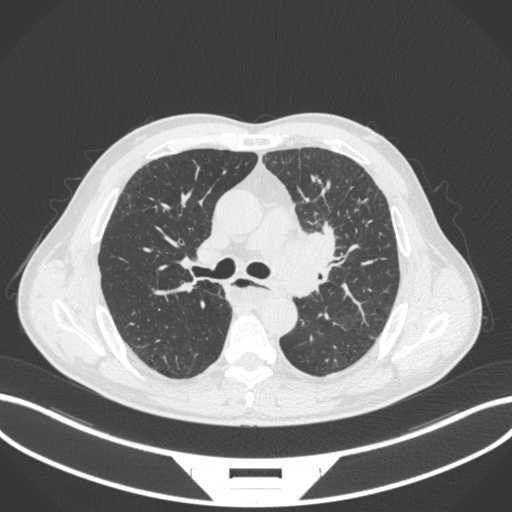
Chest CT, one axial slice; slice 239 of 411 in the series (ordered by position); 120 kVp; lung window (W 1500 / L -600 HU); 512 × 512 image matrix, field of view 400 × 400 mm. Male patient, age 57 years. Case-level facts recorded for this patient, not image findings: clinical TNM (as recorded): T2a N1 M0.
Annotated regions visible in this slice (rectangle marked by the reading radiologist):
- lung tumour (recorded histology: squamous cell carcinoma): box from (x=273, y=223) to (x=346, y=295) px